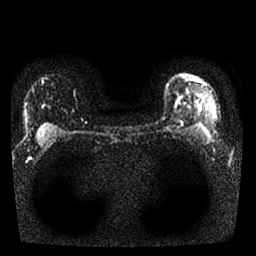
Breast MRI, one axial slice; slice 21 of 25 in the series (ordered by position); diffusion-weighted series; image 2 of 4 stored at this slice position (different b-values; order by instance number); 1.5 T; 256 × 256 image matrix, field of view 310 × 310 mm. Female patient.
Outlined on this slice (outlined manually by an expert reader):
- tumour on diffusion-weighted imaging: bounding box (x1, y1, x2, y2) in pixels: (171, 125, 176, 128)